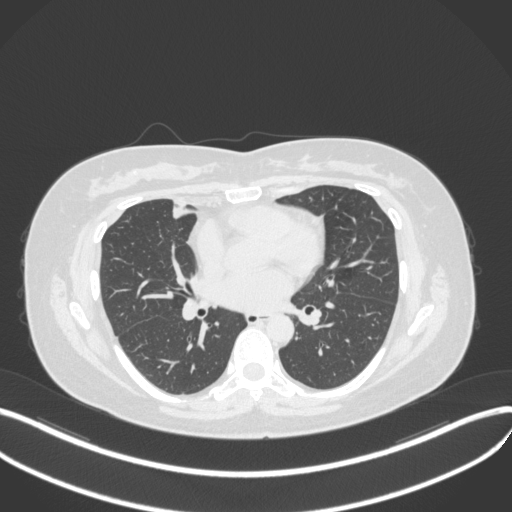
Chest CT, one axial slice. Slice 153 of 272 in the series (ordered by position). Lung window (W 1500 / L -600 HU). 1 mm slice thickness. 512 × 512 image matrix. Female patient, age 42 years. Case-level facts recorded for this patient, not image findings: clinical TNM (as recorded): T1b N0 M0.
Outlined on this slice (bounding box drawn by a radiologist):
- lung tumour (recorded histology: adenocarcinoma): bounding box <166,200,196,223> (left, top, right, bottom; pixels)